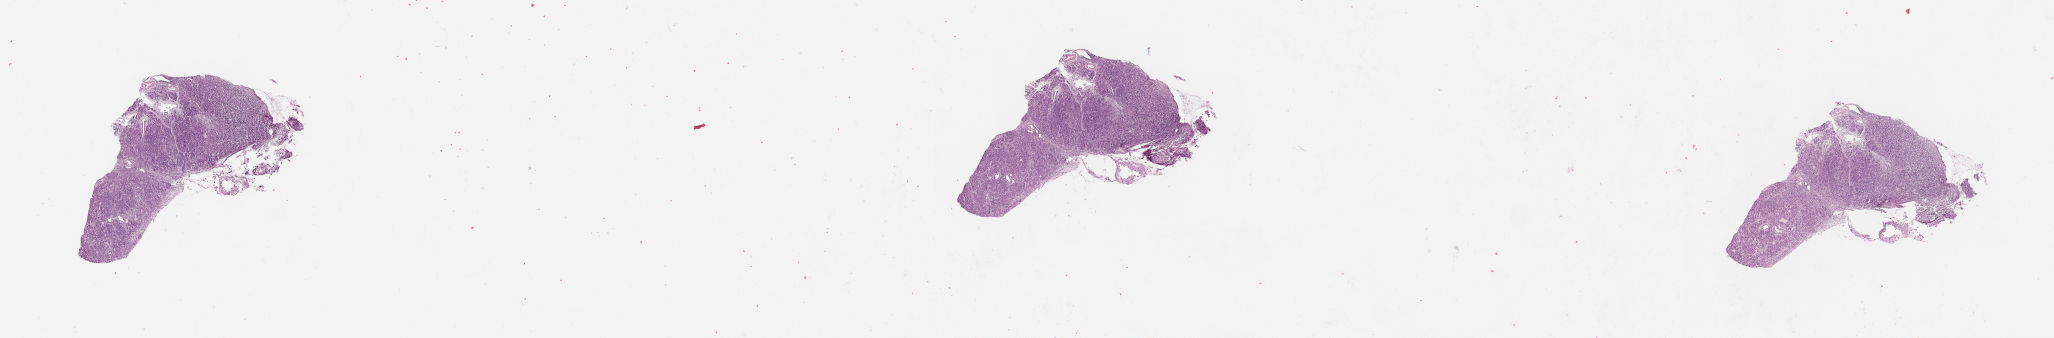
H&E-stained whole-slide image, whole scanned area (about 33.1 x 5.4 mm, acquisition: 20x scan) shown as a low-resolution overview. Normal (non-tumour) tissue sample, pancreas. Male, 75 y/o.
* this section: normal (non-tumour) tissue from the same patient
* patient diagnosis: Infiltrating duct carcinoma, NOS